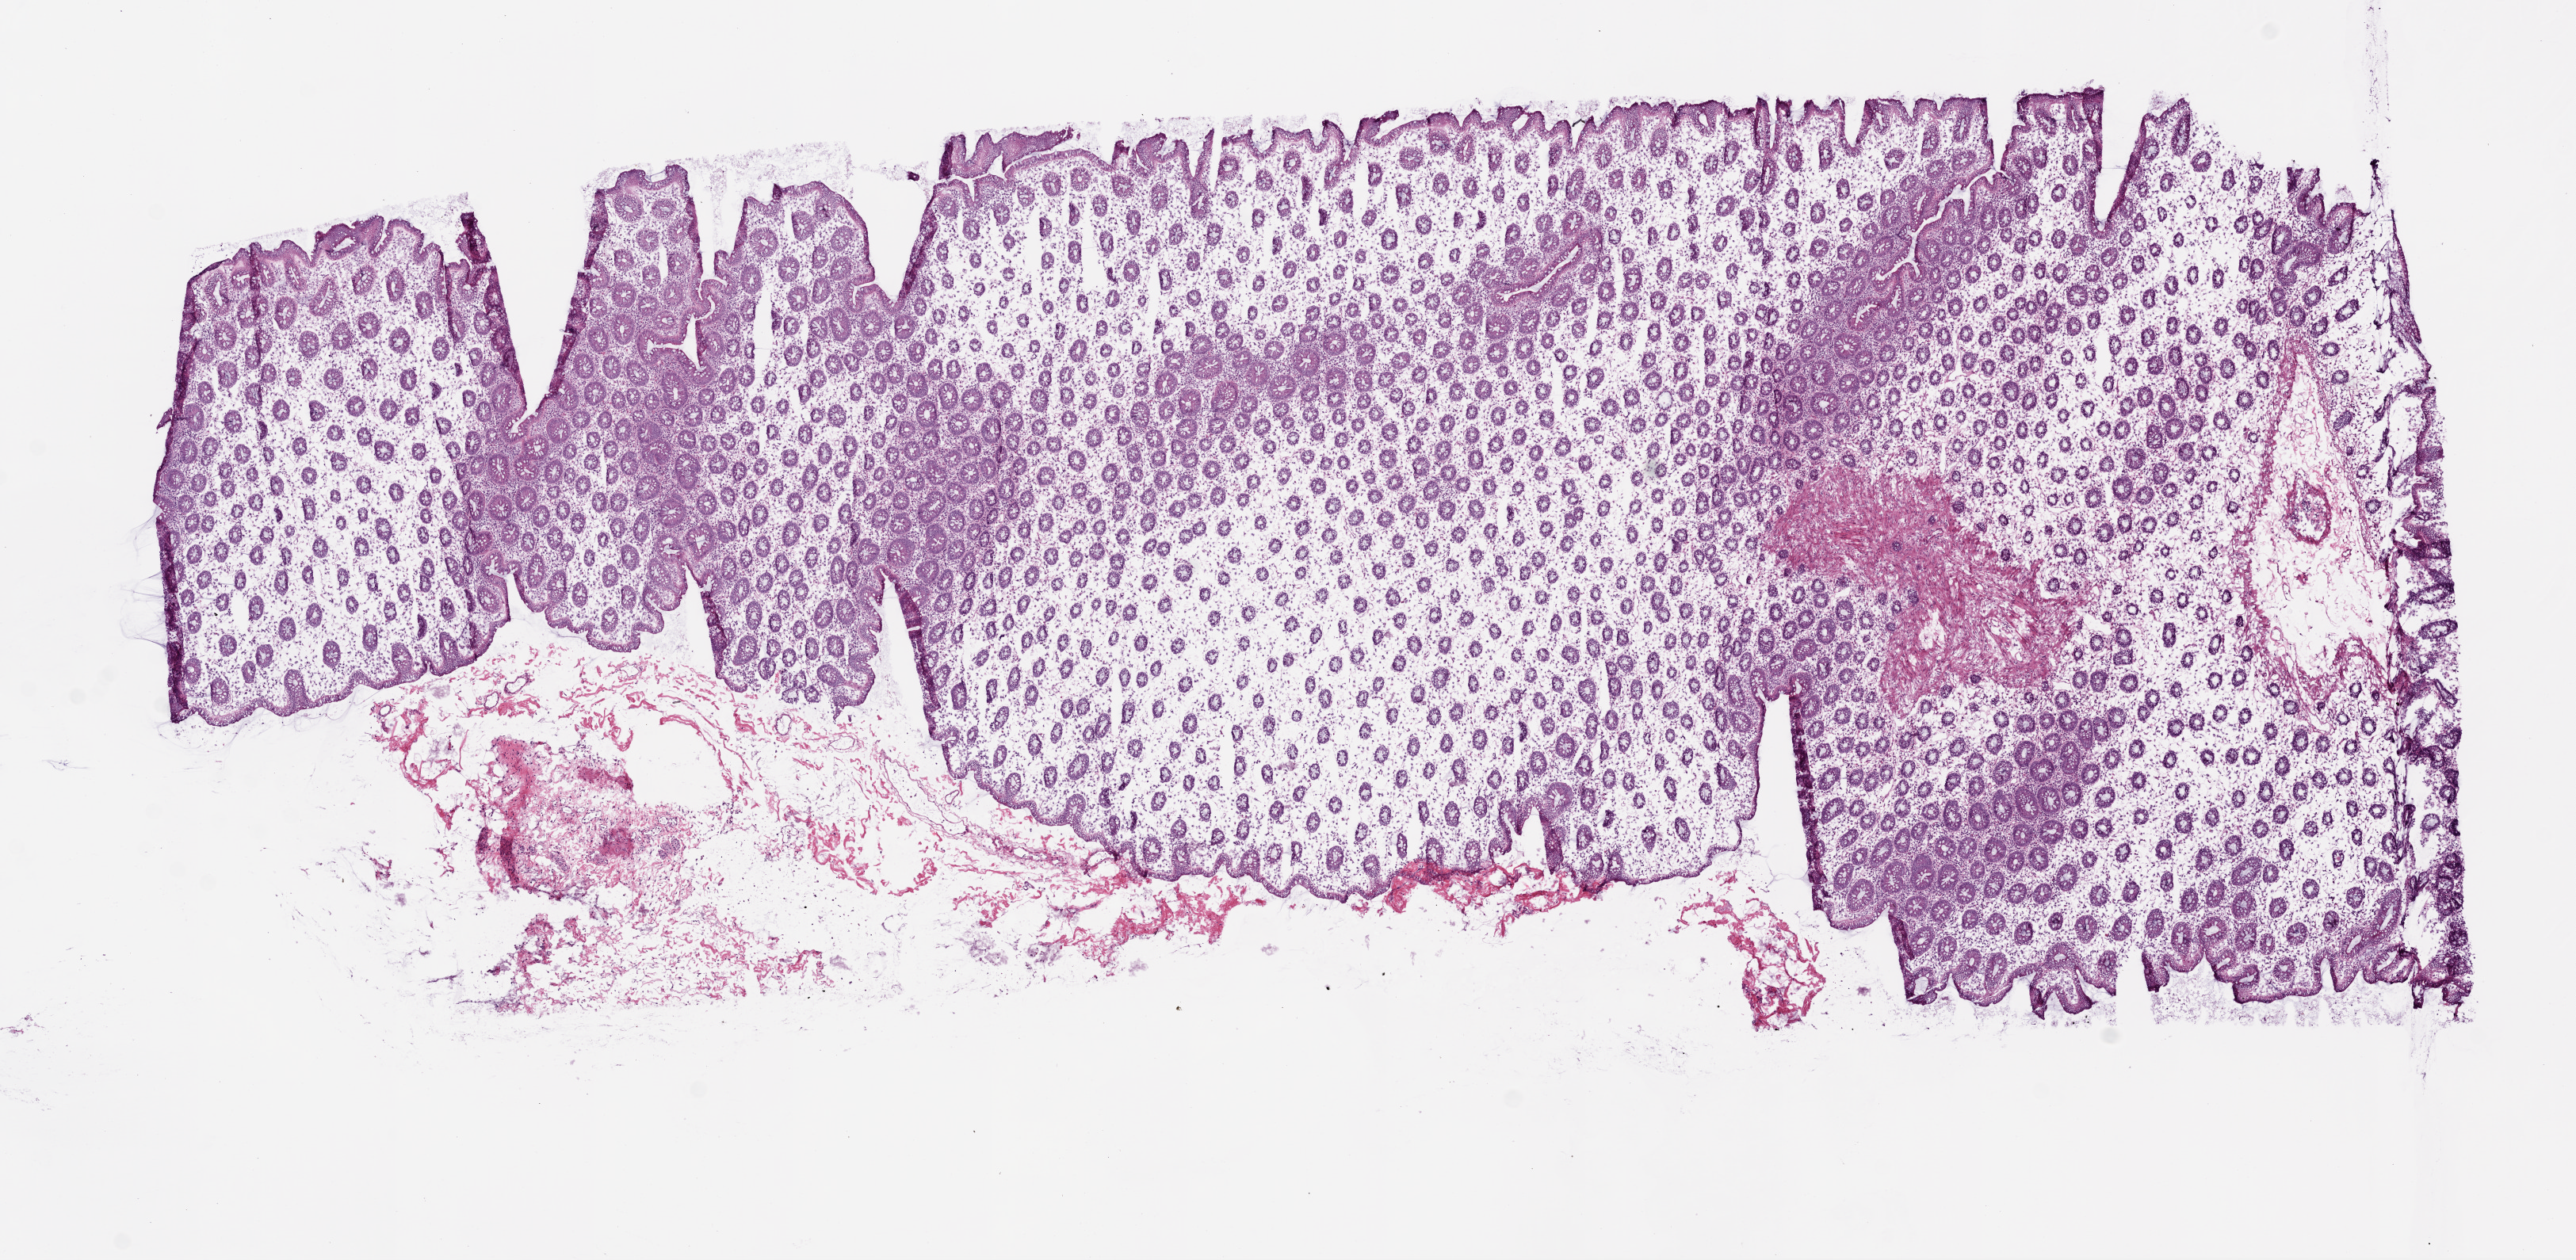
Whole-slide histology image, H&E-stained, low-resolution overview of the scanned area, about 13.0 x 6.4 mm (slide scanned at 20x); frozen section; colon, solid tissue normal (non-tumour tissue) sample. Male, age 82 years at initial diagnosis.
This section: solid tissue normal (non-tumour) sample from the same patient. Patient diagnosis: Adenocarcinoma, NOS (ascending colon).